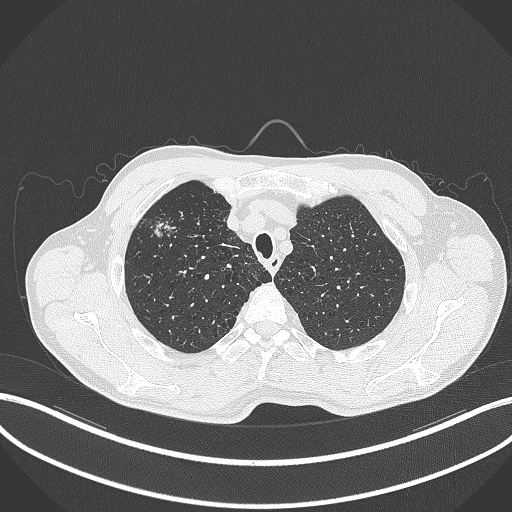
Chest CT, one axial slice; position 350 of 427 along the scan axis; reconstruction kernel B70f; lung window (W 1500 / L -600 HU); 1 mm slice thickness; 512 × 512 image matrix. Patient: male, 69 years. From the clinical record (not read from this slice): clinical TNM (as recorded): T1b N1 M0.
Structures marked on this image (bounding box drawn by a radiologist):
- lung tumour (recorded histology: adenocarcinoma): bounding box (x1, y1, x2, y2) in pixels: (148, 207, 185, 242)